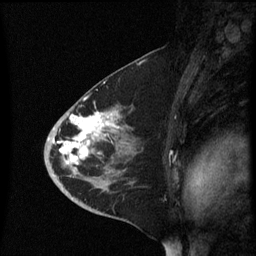
Breast MRI (dynamic contrast-enhanced), one sagittal slice; dynamic contrast-enhanced series, image 2 of 3 at this slice position (ordered by acquisition); 1.5 T; TE 4.2 ms, TR 8.4 ms; 2.3 mm slice thickness; 256 × 256 image matrix, field of view 200 × 200 mm. Female patient, age 46 years. Case-level facts recorded for this patient, not image findings: setting: breast cancer imaged before/during neoadjuvant chemotherapy; receptor status: HER2-positive.
Annotated regions visible in this slice (semi-automatically segmented with operator editing):
- analysis volume of interest (the breast-tissue region the enhancement analysis was run in; not a lesion): bounding box [x1, y1, x2, y2] px = [44, 96, 143, 187]
- tumour enhancement mask (voxels above the 70 % enhancement threshold inside the analysis volume of interest): [53, 110, 117, 173]